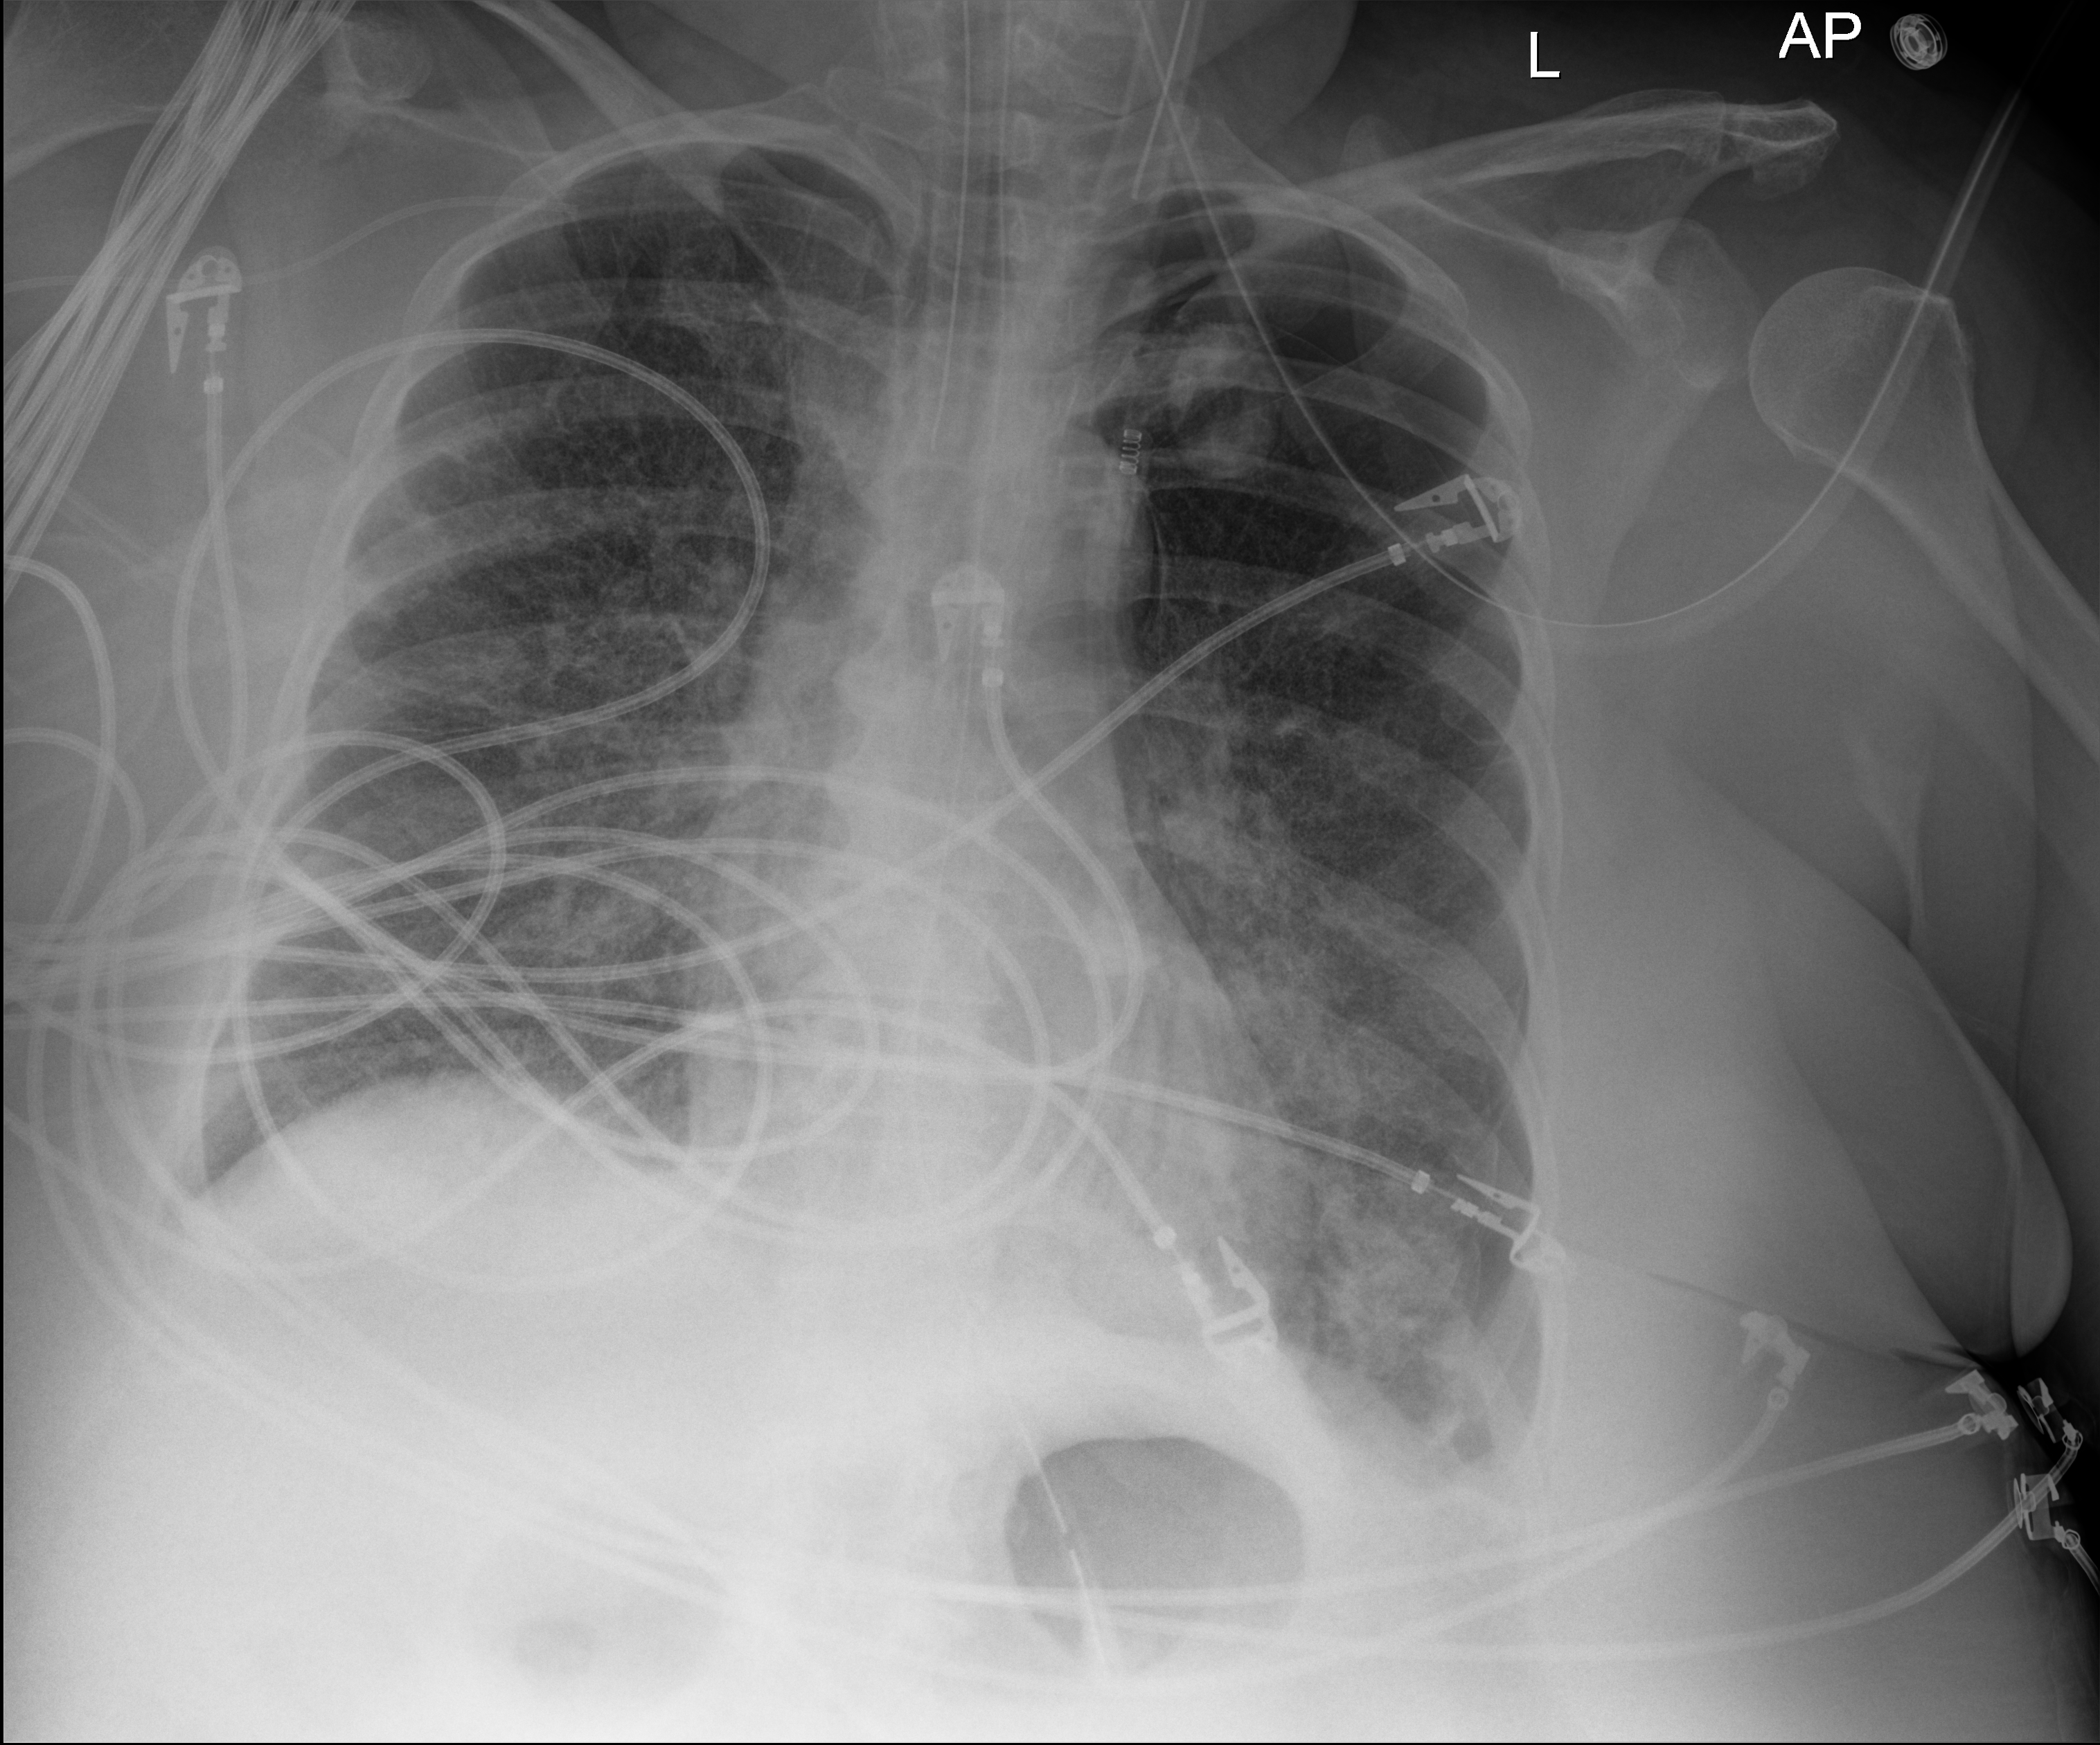
Bedside chest radiograph (digital radiography); anteroposterior (AP) projection. Patient hospitalised with COVID-19; female, aged 60–74 years.
Hospital-stay facts (about this admission, not read from this image; timing relative to this image not recorded): admitted to intensive care during this hospital stay: yes; hypertension (admission record): no; mechanically ventilated during this hospital stay: yes.